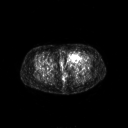
FDG PET of an extremity soft-tissue mass (from a PET/CT study), one axial slice. Slice 39 of 267 in the series (ordered by position). 3.27 mm slice thickness. 128 × 128 image matrix, field of view 700 × 700 mm. Female patient, age 47 years. Case-level facts recorded for this patient, not image findings: histological type: myxofibrosarcoma; grade: intermediate; site of the primary tumour: left thigh.
Structures marked on this image (expert contour drawn on MRI and transferred to this co-registered scan by the dataset authors):
- gross tumour volume including surrounding oedema: bounding box <65,52,83,64> (left, top, right, bottom; pixels)
- gross tumour volume (mass): <67,52,80,62>